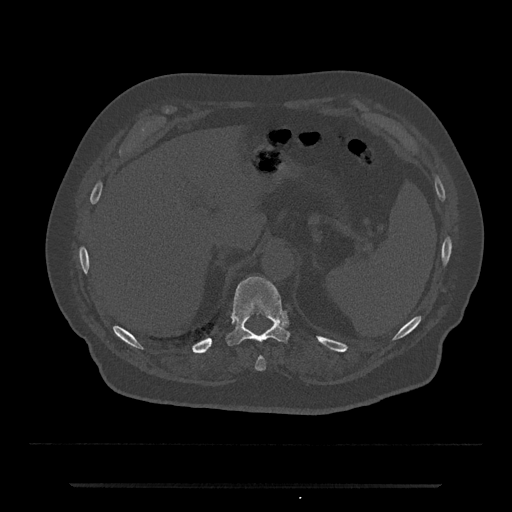
CT including the spine, one axial slice; position 656 of 797 along the scan axis; reconstruction kernel Br40s/3; 120 kVp; bone window (W 1800 / L 400 HU); 512 × 512 image matrix, field of view 434 × 434 mm. Male patient, age 80 years. Case-level facts recorded for this patient, not image findings: primary cancer: prostate.
Annotated regions visible in this slice (semi-automatically segmented with operator editing):
- T10 vertebra: box from (x=255, y=356) to (x=266, y=371) px
- T11 vertebra: (x=226, y=276)–(x=290, y=345)